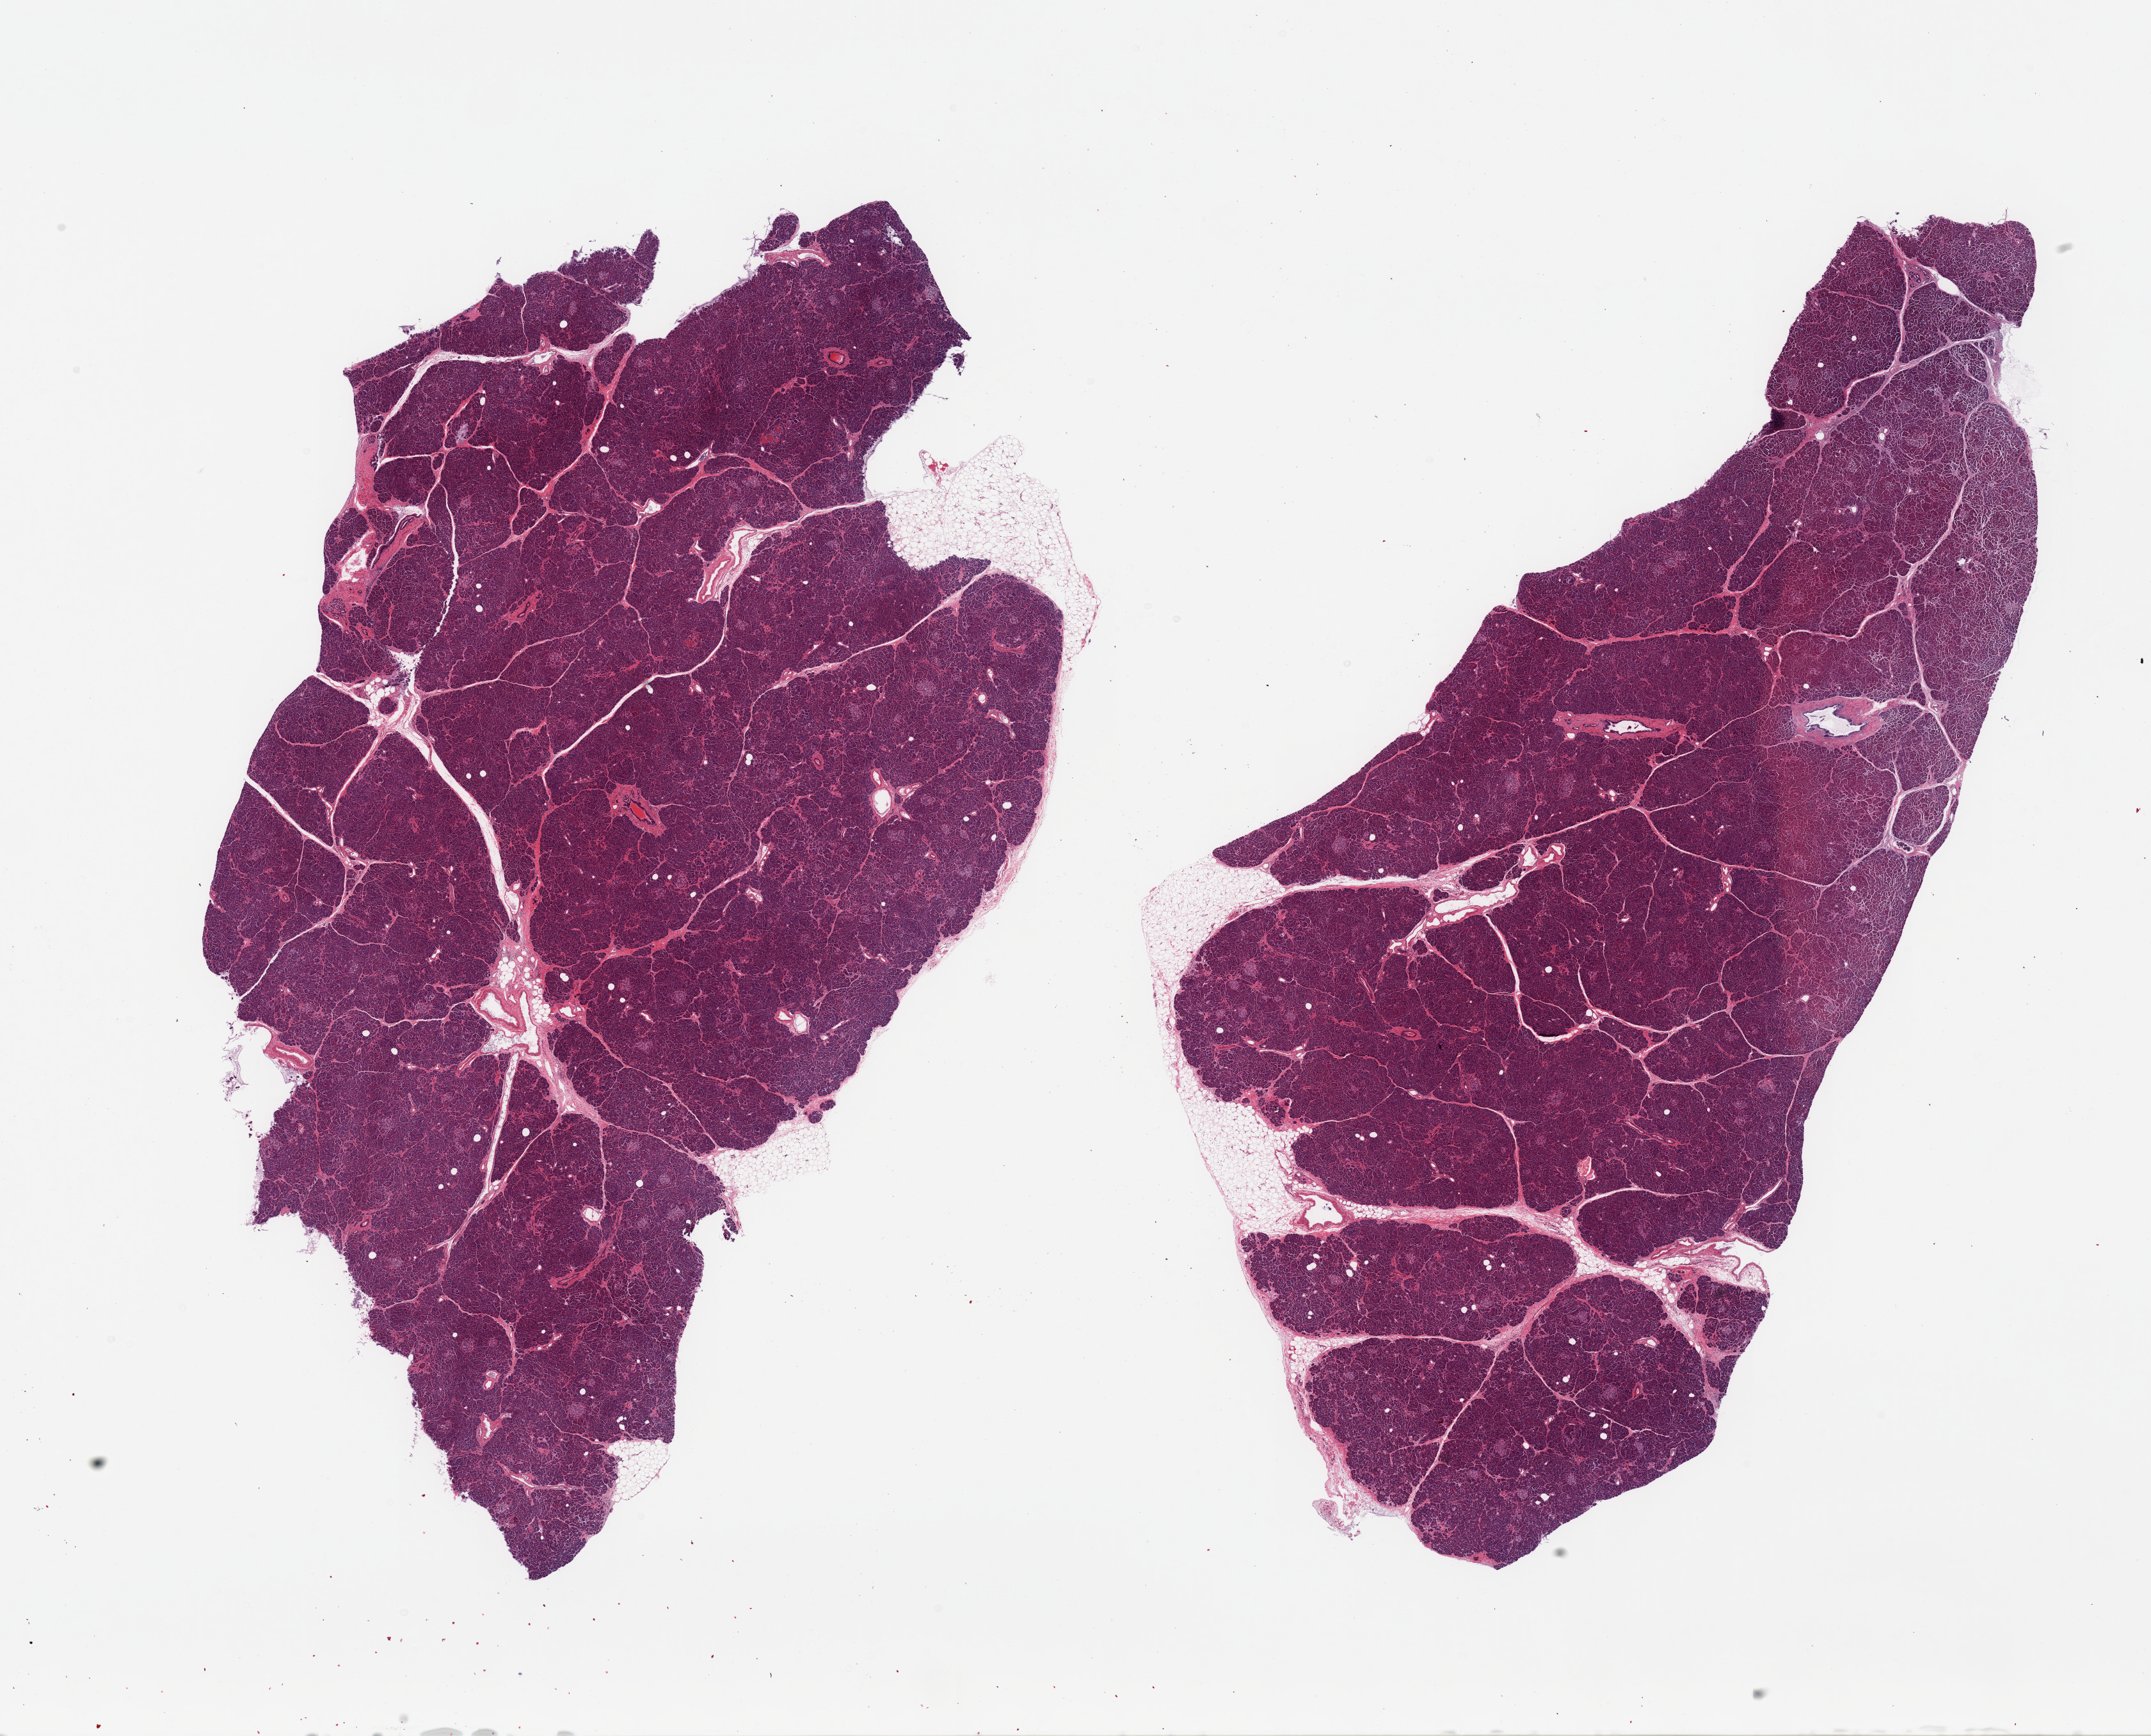
Digitized haematoxylin and eosin-stained section — shown as a low-resolution overview of the whole scanned area (about 26.6 x 21.5 mm), PAXgene-fixed, paraffin-embedded tissue, section of pancreas (target tissue), donor tissue sample. Female donor.
Pathologist's review note for this sample: 2 pieces, focally approaching score 2 for autolysis; Islets well-preserved; Focal adherent fat, ~2mm.